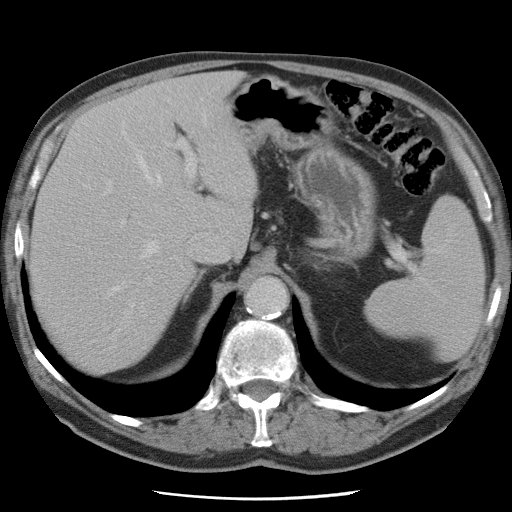
Contrast-enhanced abdominal CT, one axial slice. Intravenous contrast given. Soft-tissue window (W 400 / L 40 HU). 5 mm slice thickness. 512 × 512 image matrix, field of view 337 × 337 mm. Male patient, age 75 years. From the clinical record (not read from this slice): diagnosis: colorectal cancer liver metastases, imaged before liver resection; multiple liver metastases: yes.
Annotated regions visible in this slice (outlined manually by an expert reader):
- hepatic veins: bounding box <57,112,206,316> (left, top, right, bottom; pixels)
- liver: <32,71,253,369>
- planned liver remnant (the part of the liver to remain after resection): <31,127,194,368>
- portal vein (with intrahepatic branches): <106,139,195,229>